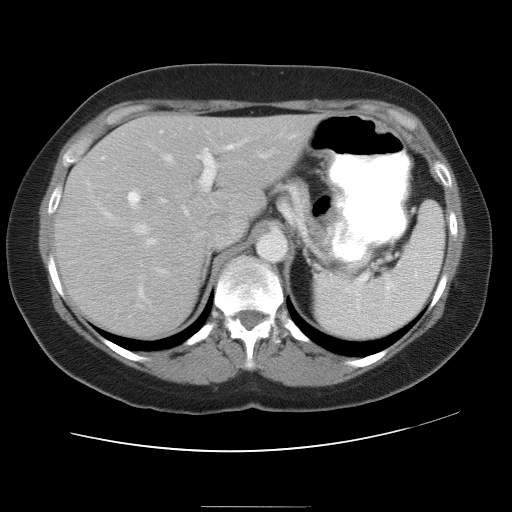
Contrast-enhanced abdominal CT, one axial slice; reconstruction kernel STANDARD; 120 kVp; soft-tissue window (W 400 / L 40 HU); 7.5 mm slice thickness; 512 × 512 image matrix. Female patient, age 52 years. From the clinical record (not read from this slice): diagnosis: colorectal cancer liver metastases, imaged before liver resection; multiple liver metastases: no; largest metastasis: 3 cm; disease in both lobes: yes.
Structures marked on this image (outlined manually by an expert reader):
- hepatic veins: bounding box <81,155,265,234> (left, top, right, bottom; pixels)
- liver: <54,115,317,339>
- planned liver remnant (the part of the liver to remain after resection): <143,116,318,217>
- portal vein (with intrahepatic branches): <128,138,248,302>